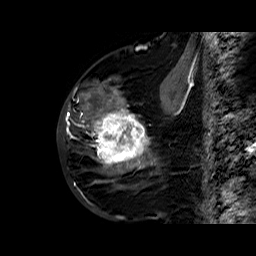
Breast MRI (dynamic contrast-enhanced), one sagittal slice; slice 22 of 60 in the series (ordered by position); dynamic contrast-enhanced series, time point 2 of 6 at this slice position (early post-contrast); 1.5 T; TE 6.4 ms, TR 32.8 ms; 256 × 256 image matrix, field of view 200 × 200 mm. Female patient. From the clinical record (not read from this slice): setting: breast cancer imaged before/during neoadjuvant chemotherapy; receptor status: HR-positive, HER2-negative.
Outlined on this slice (semi-automatically segmented with operator editing):
- analysis volume of interest (the breast-tissue region the enhancement analysis was run in; not a lesion): bounding box (x1, y1, x2, y2) in pixels: (86, 77, 163, 177)
- tumour enhancement mask (voxels above the 100 % enhancement threshold inside the analysis volume of interest): (86, 88, 153, 169)